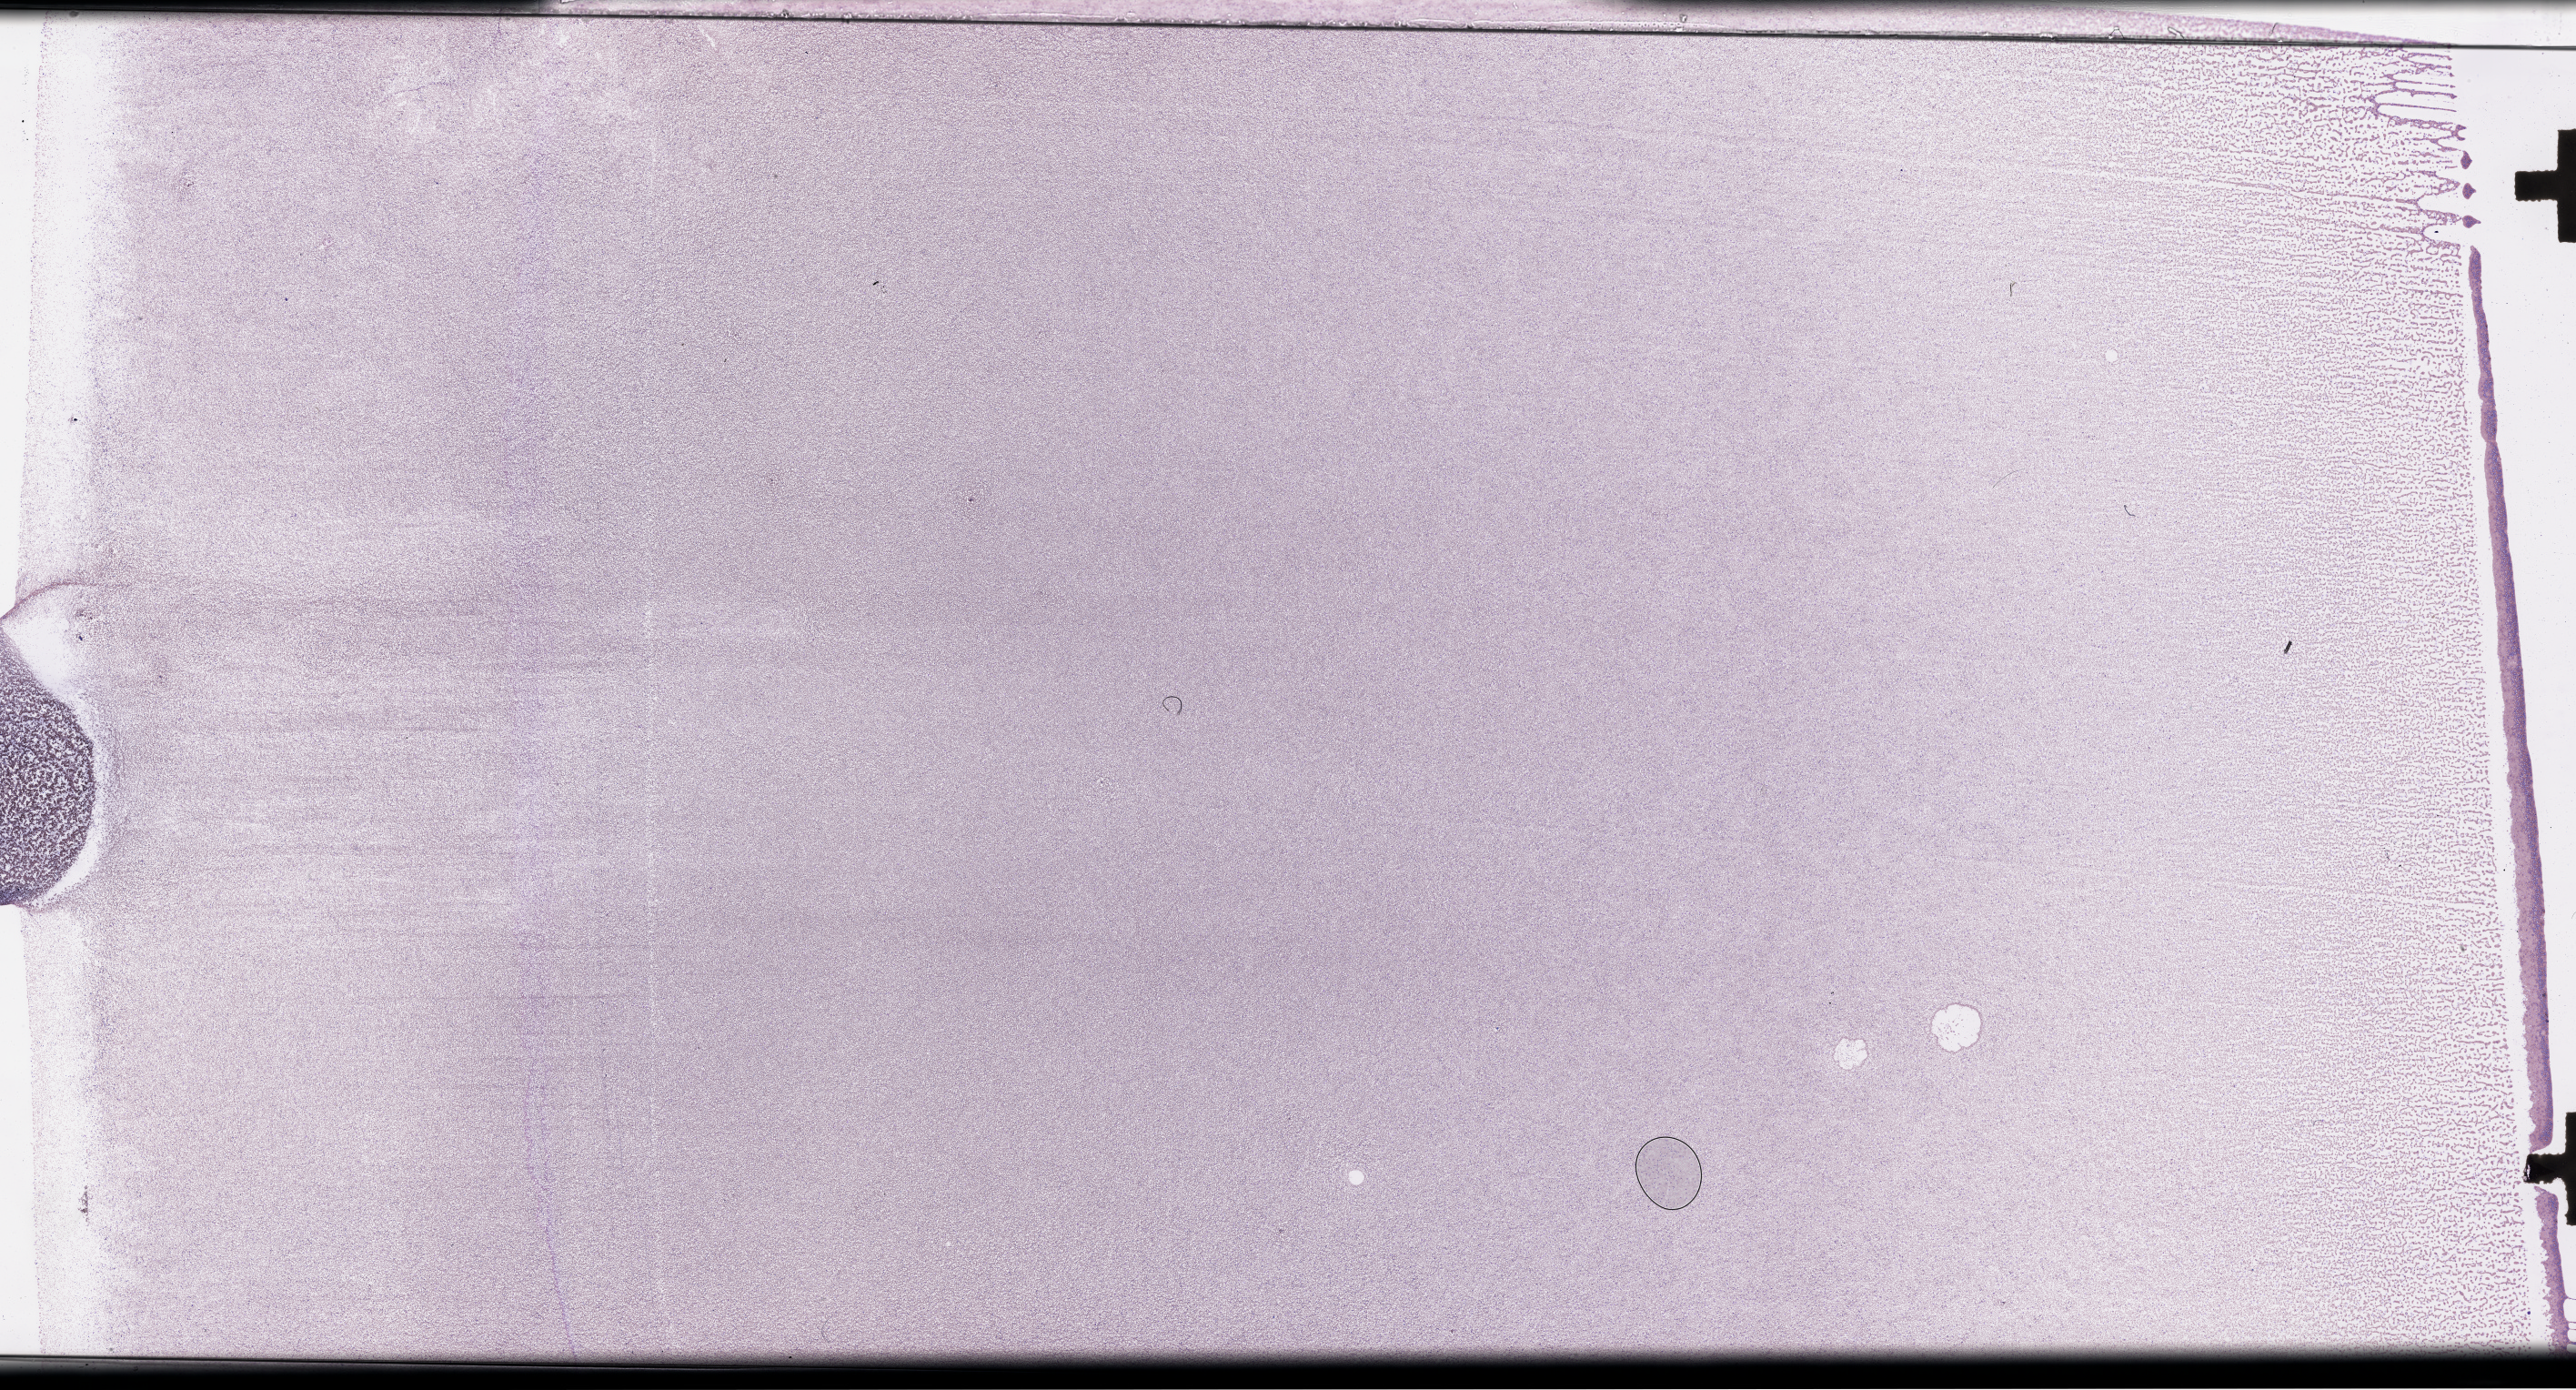
Digitized Hematoxylin and eosin (H&E) stained tissue section (whole slide), shown as a low-resolution overview of the whole scanned area (about 45.7 x 24.7 mm). Peripheral blood (leukaemic) sample. 19-year-old male patient.
- WHO classification: AML with myelodysplasia-related changes
- diagnosis: Acute Myeloid Leukemia
- FAB classification: M1